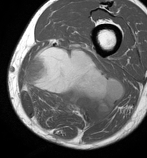
MRI of an extremity soft-tissue mass, one axial slice. Position 36 of 86 along the scan axis. MR volume resampled by the dataset authors to the PET/CT grid (not the native acquisition matrix). 3.27 mm slice thickness. 147 × 158 image matrix, field of view 144 × 154 mm. Male patient. From the clinical record (not read from this slice): histological type: undifferentiated pleomorphic liposarcoma; grade: high; site of the primary tumour: left thigh.
Outlined on this slice (expert contour drawn on MRI and transferred to this co-registered scan by the dataset authors):
- gross tumour volume including surrounding oedema: bounding box <25,42,125,127> (left, top, right, bottom; pixels)
- gross tumour volume (mass): <25,47,125,127>